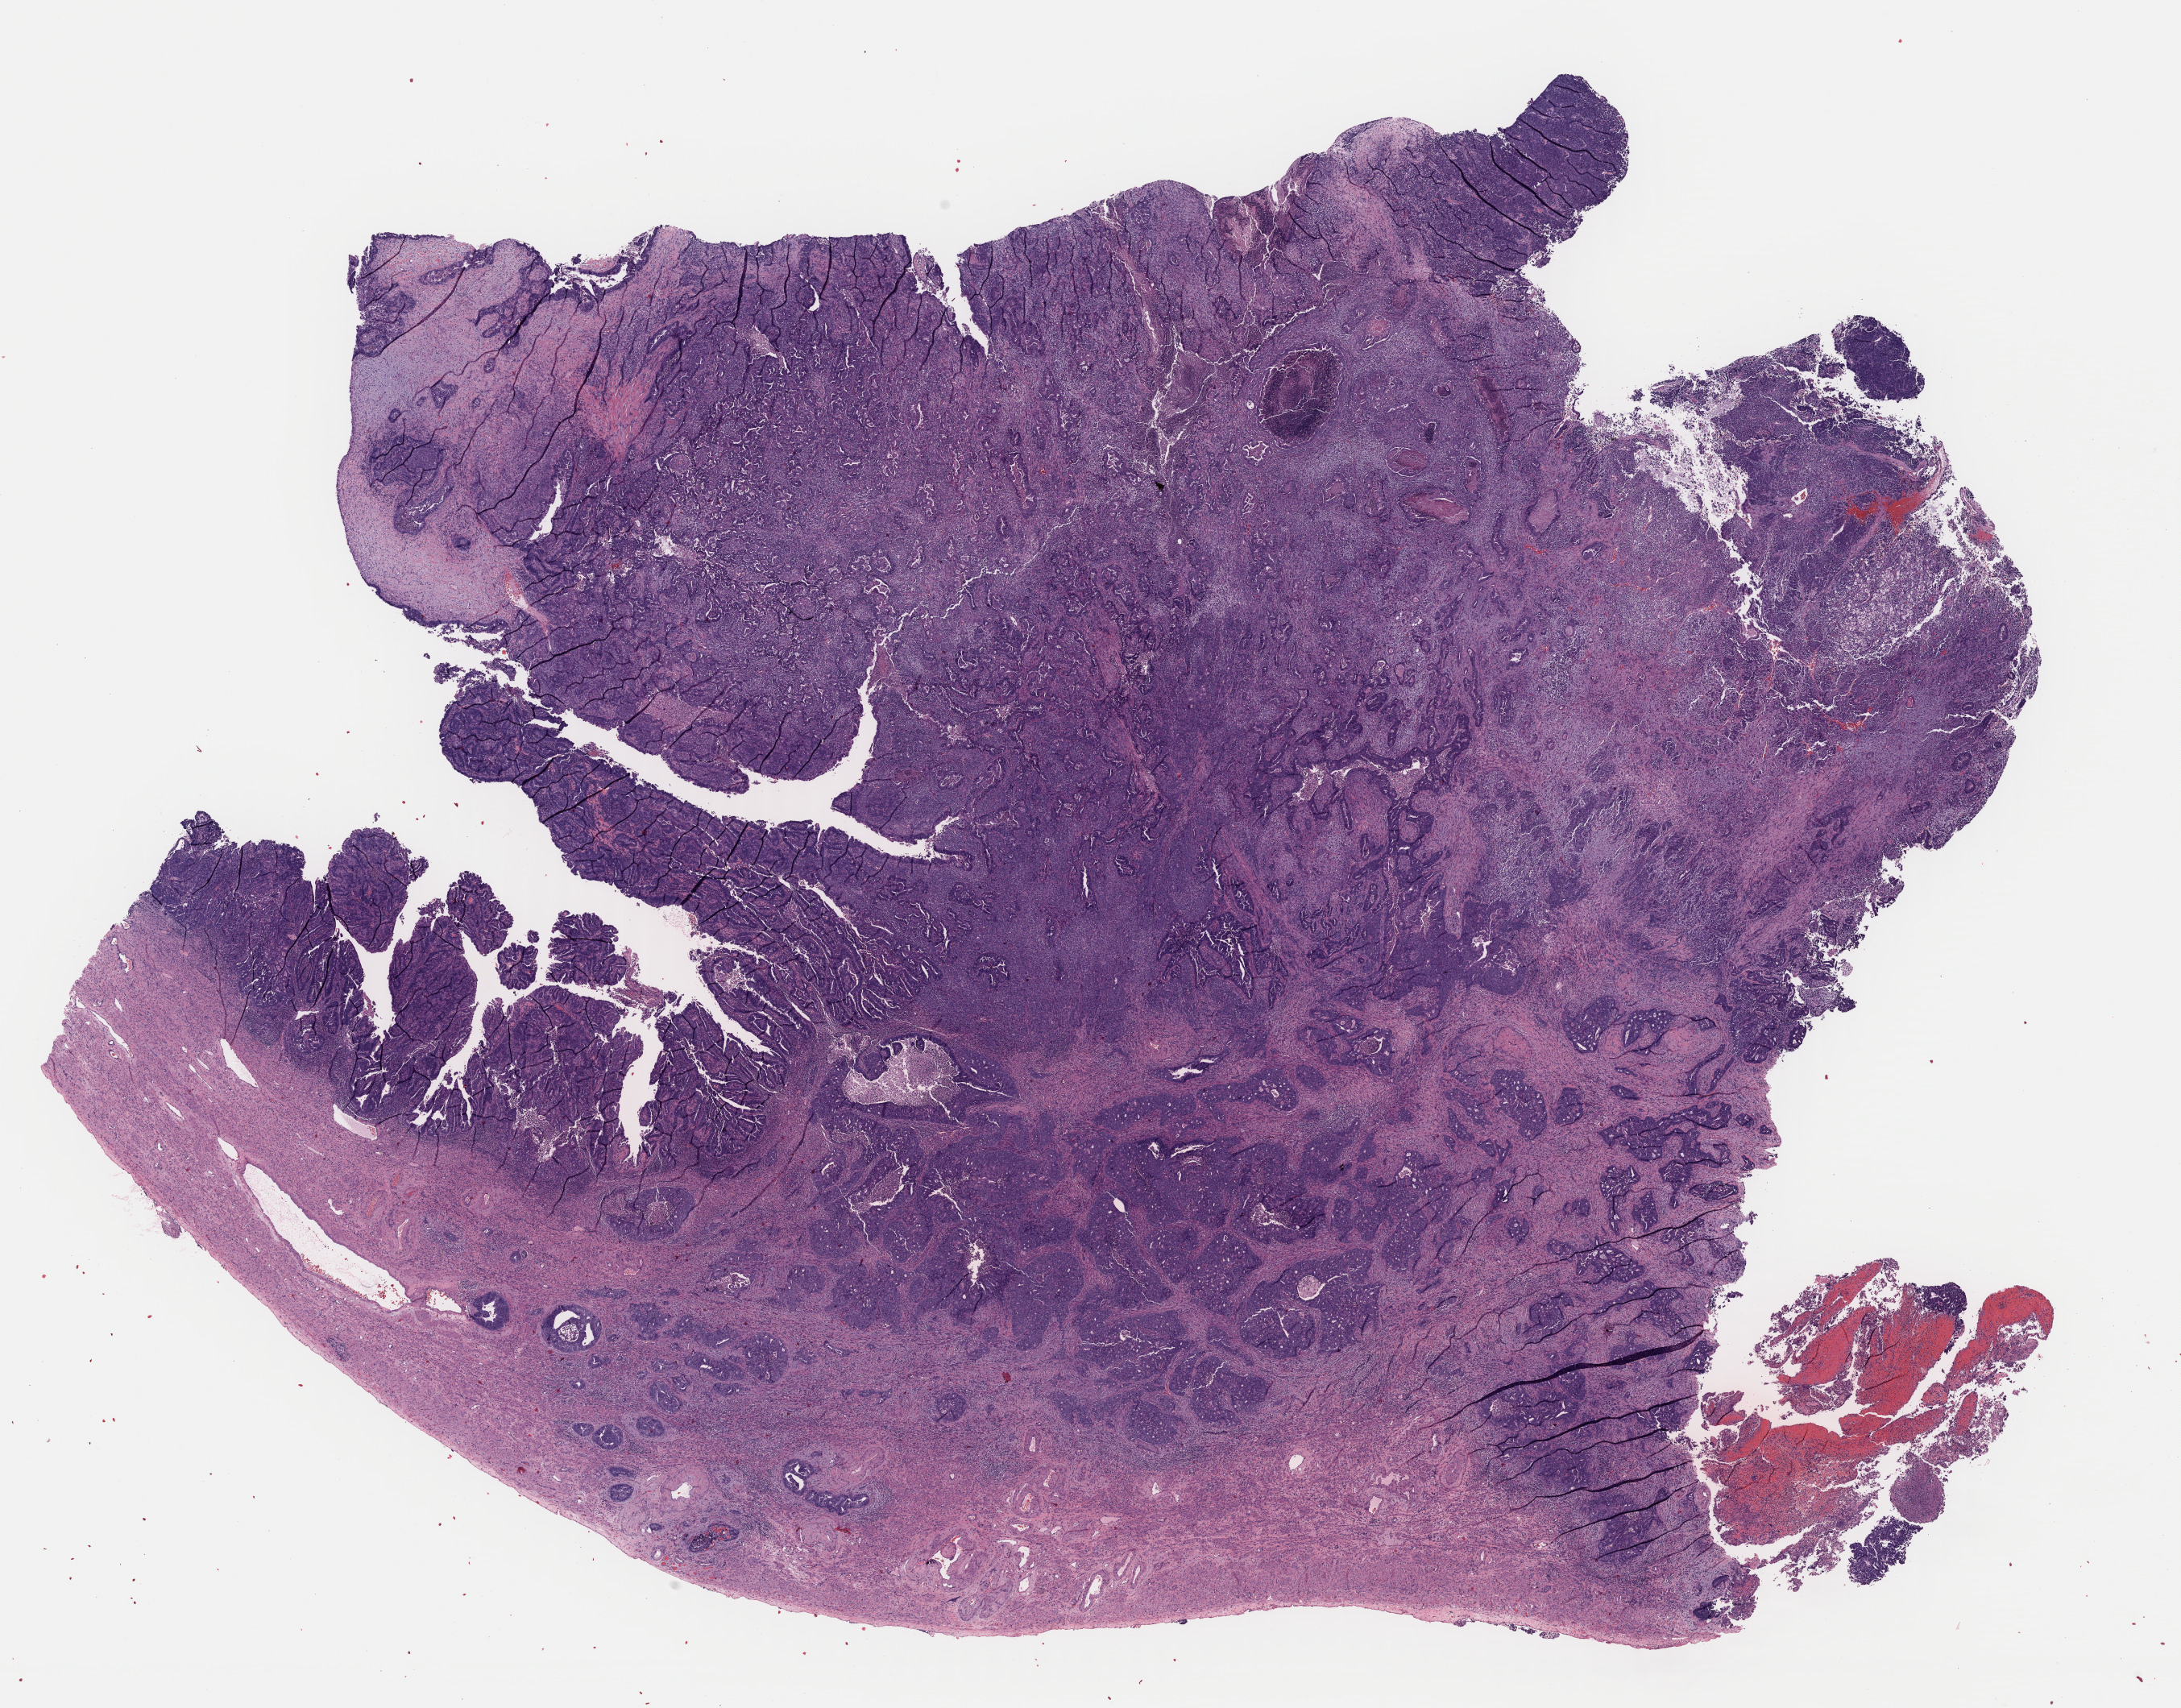
H&E whole-slide image, whole scanned area (about 21.4 x 16.7 mm) shown as a low-resolution overview, formalin-fixed paraffin-embedded (FFPE) diagnostic section, sample: primary tumour, uterus. Female, age 81 years at initial diagnosis.
FIGO stage: IIIA. Pathologic diagnosis: Mullerian mixed tumor.